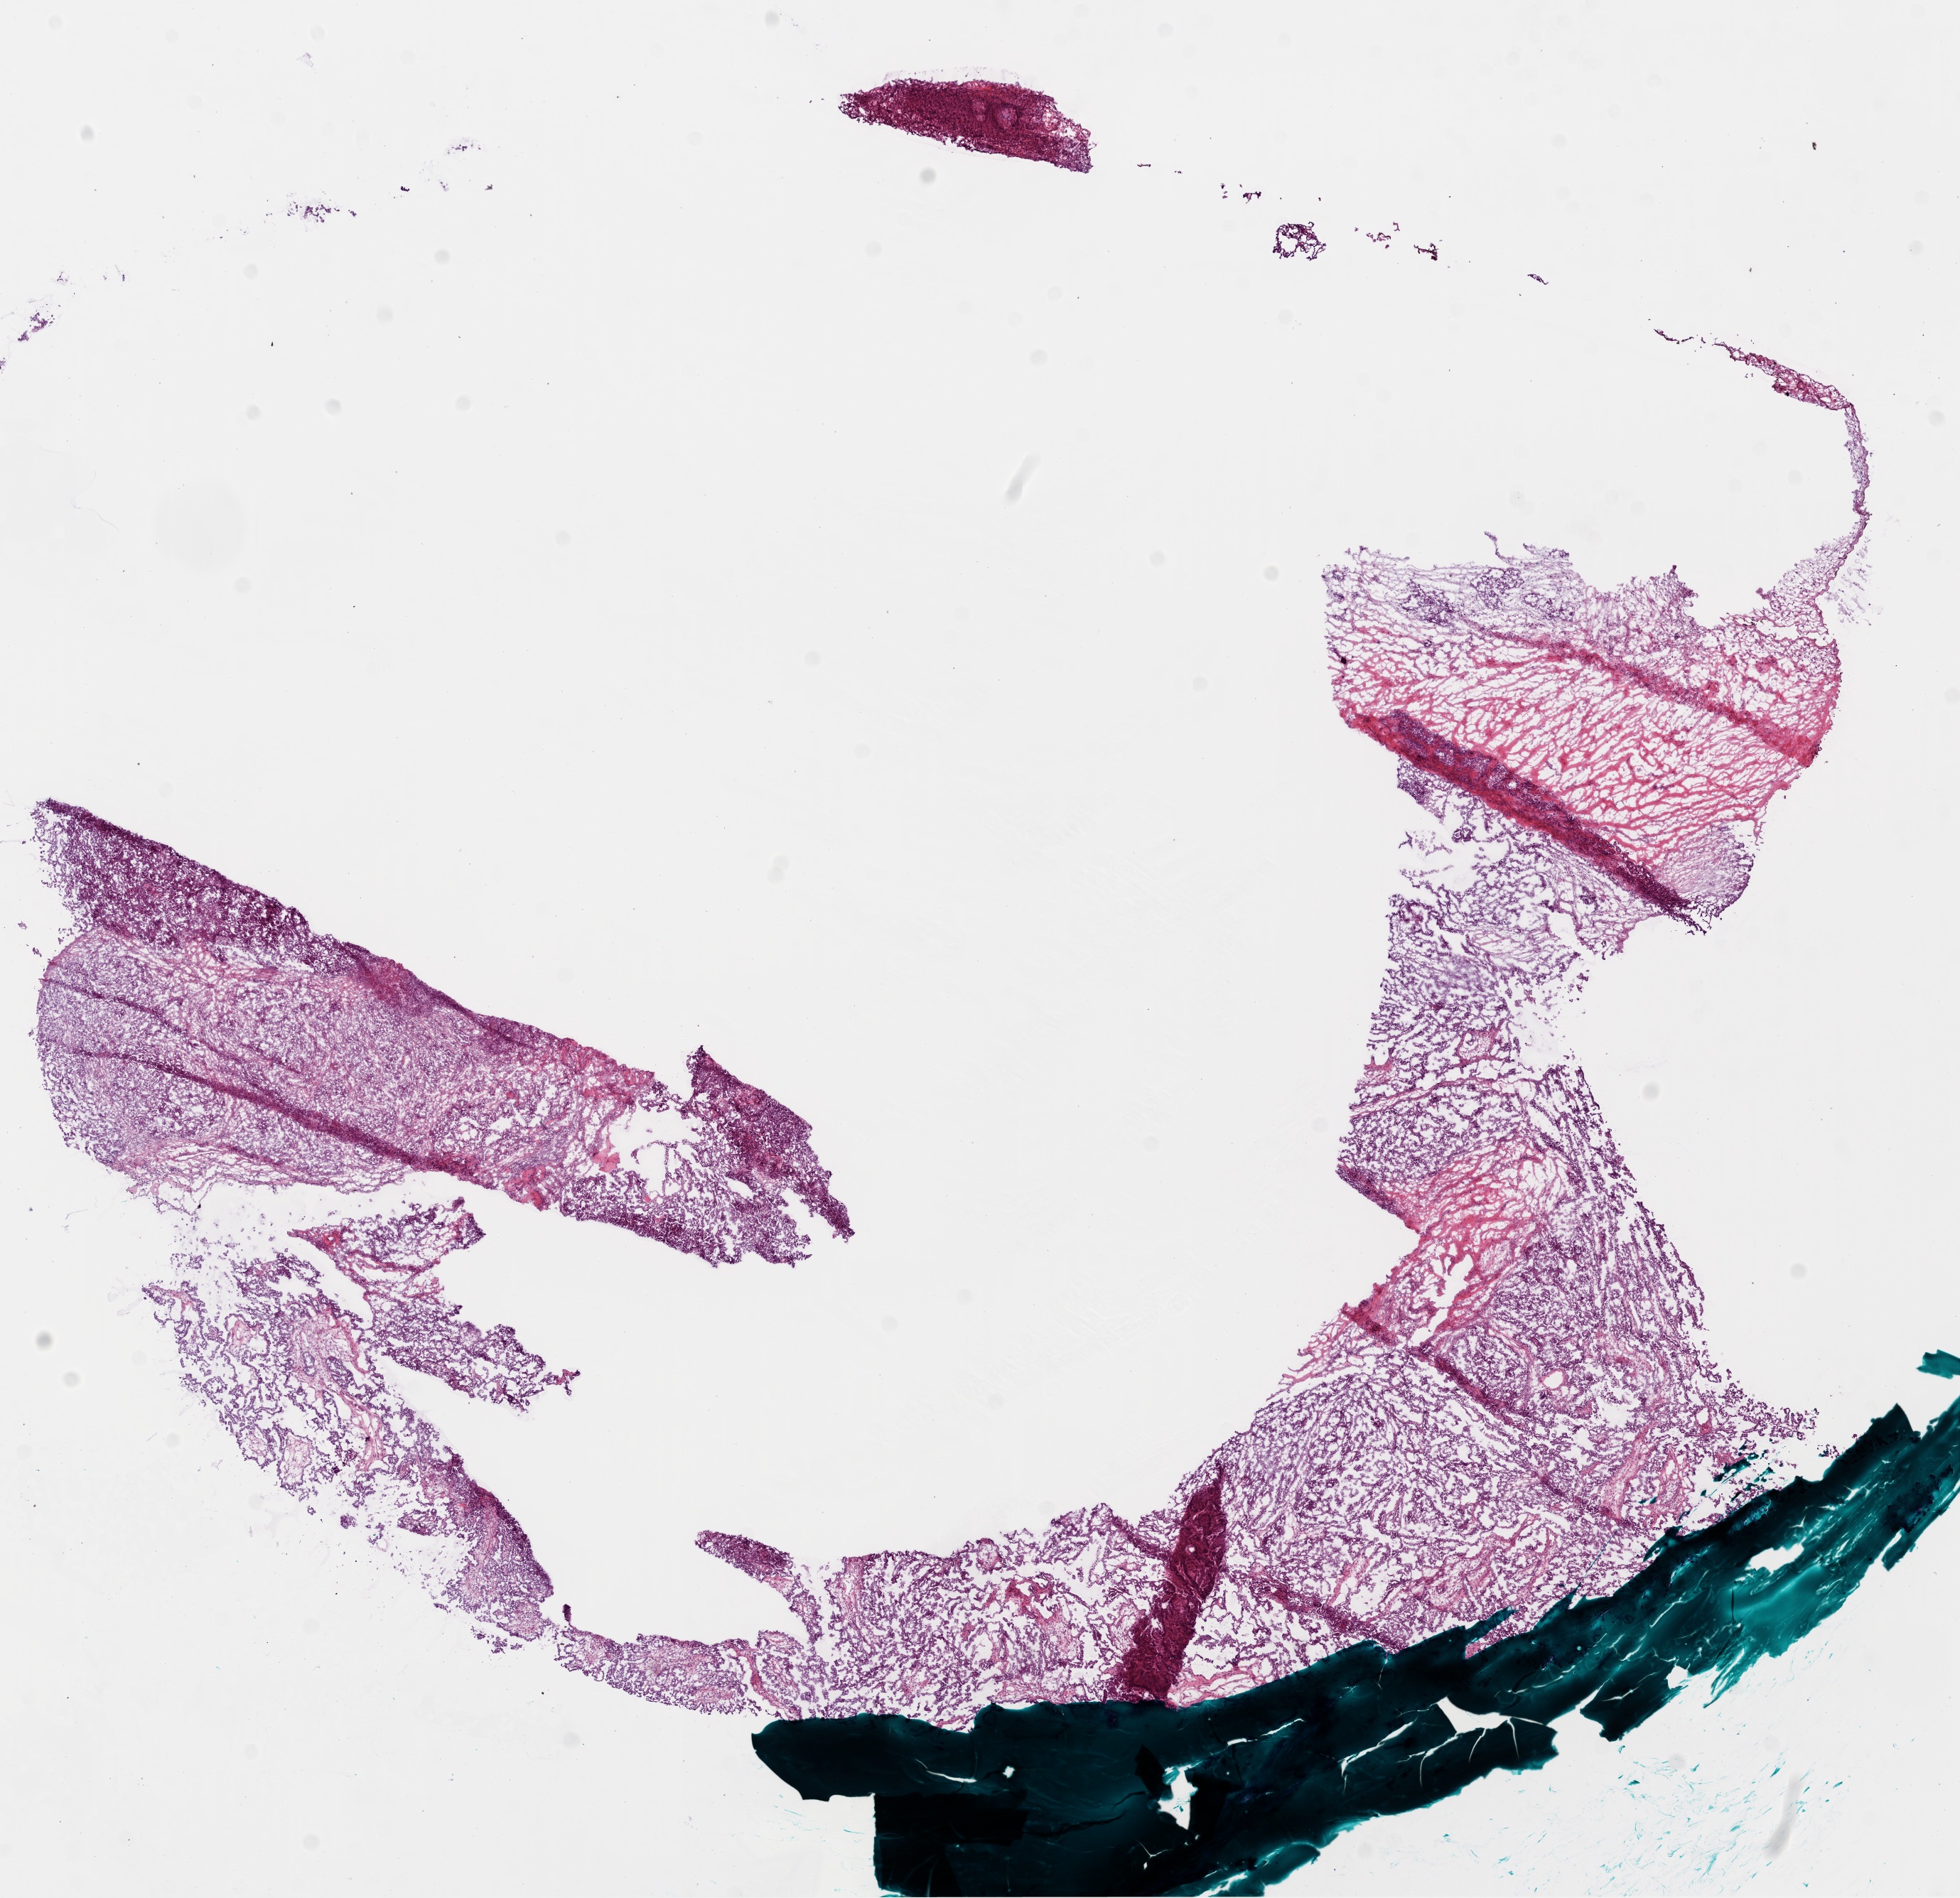
Digitized Hematoxylin and eosin (H&E) stained tissue section (whole slide) — a low-resolution overview of the entire scanned area, about 11.1 x 10.8 mm, frozen section from the bottom of the tissue portion, sample: primary tumour, ovary. Female, age 75 years at initial diagnosis. Histologic grade: G3 (poorly differentiated). Pathologist review of this section (percent, as recorded): tumour cells 89%, tumour nuclei 90%, normal cells 10%, necrosis 1%.
Histologic diagnosis: Serous cystadenocarcinoma, NOS. FIGO stage: IV.